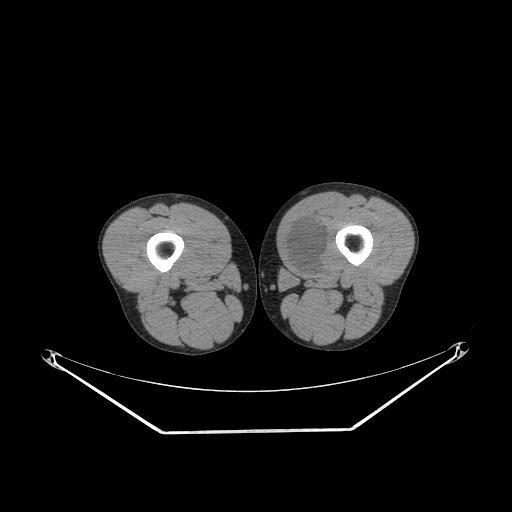
CT of an extremity soft-tissue mass (from a PET/CT study), one axial slice. Slice 235 of 311 in the series (ordered by position). Reconstruction kernel SOFT. Soft-tissue window (W 400 / L 40 HU). 3.75 mm slice thickness. 512 × 512 image matrix, field of view 500 × 500 mm. Male patient. Case-level facts recorded for this patient, not image findings: histological type: mixoid liposarcoma; grade: low; site of the primary tumour: left thigh.
Outlined on this slice (expert contour drawn on MRI and transferred to this co-registered scan by the dataset authors):
- gross tumour volume (mass): bounding box [x1, y1, x2, y2] px = [285, 219, 328, 277]